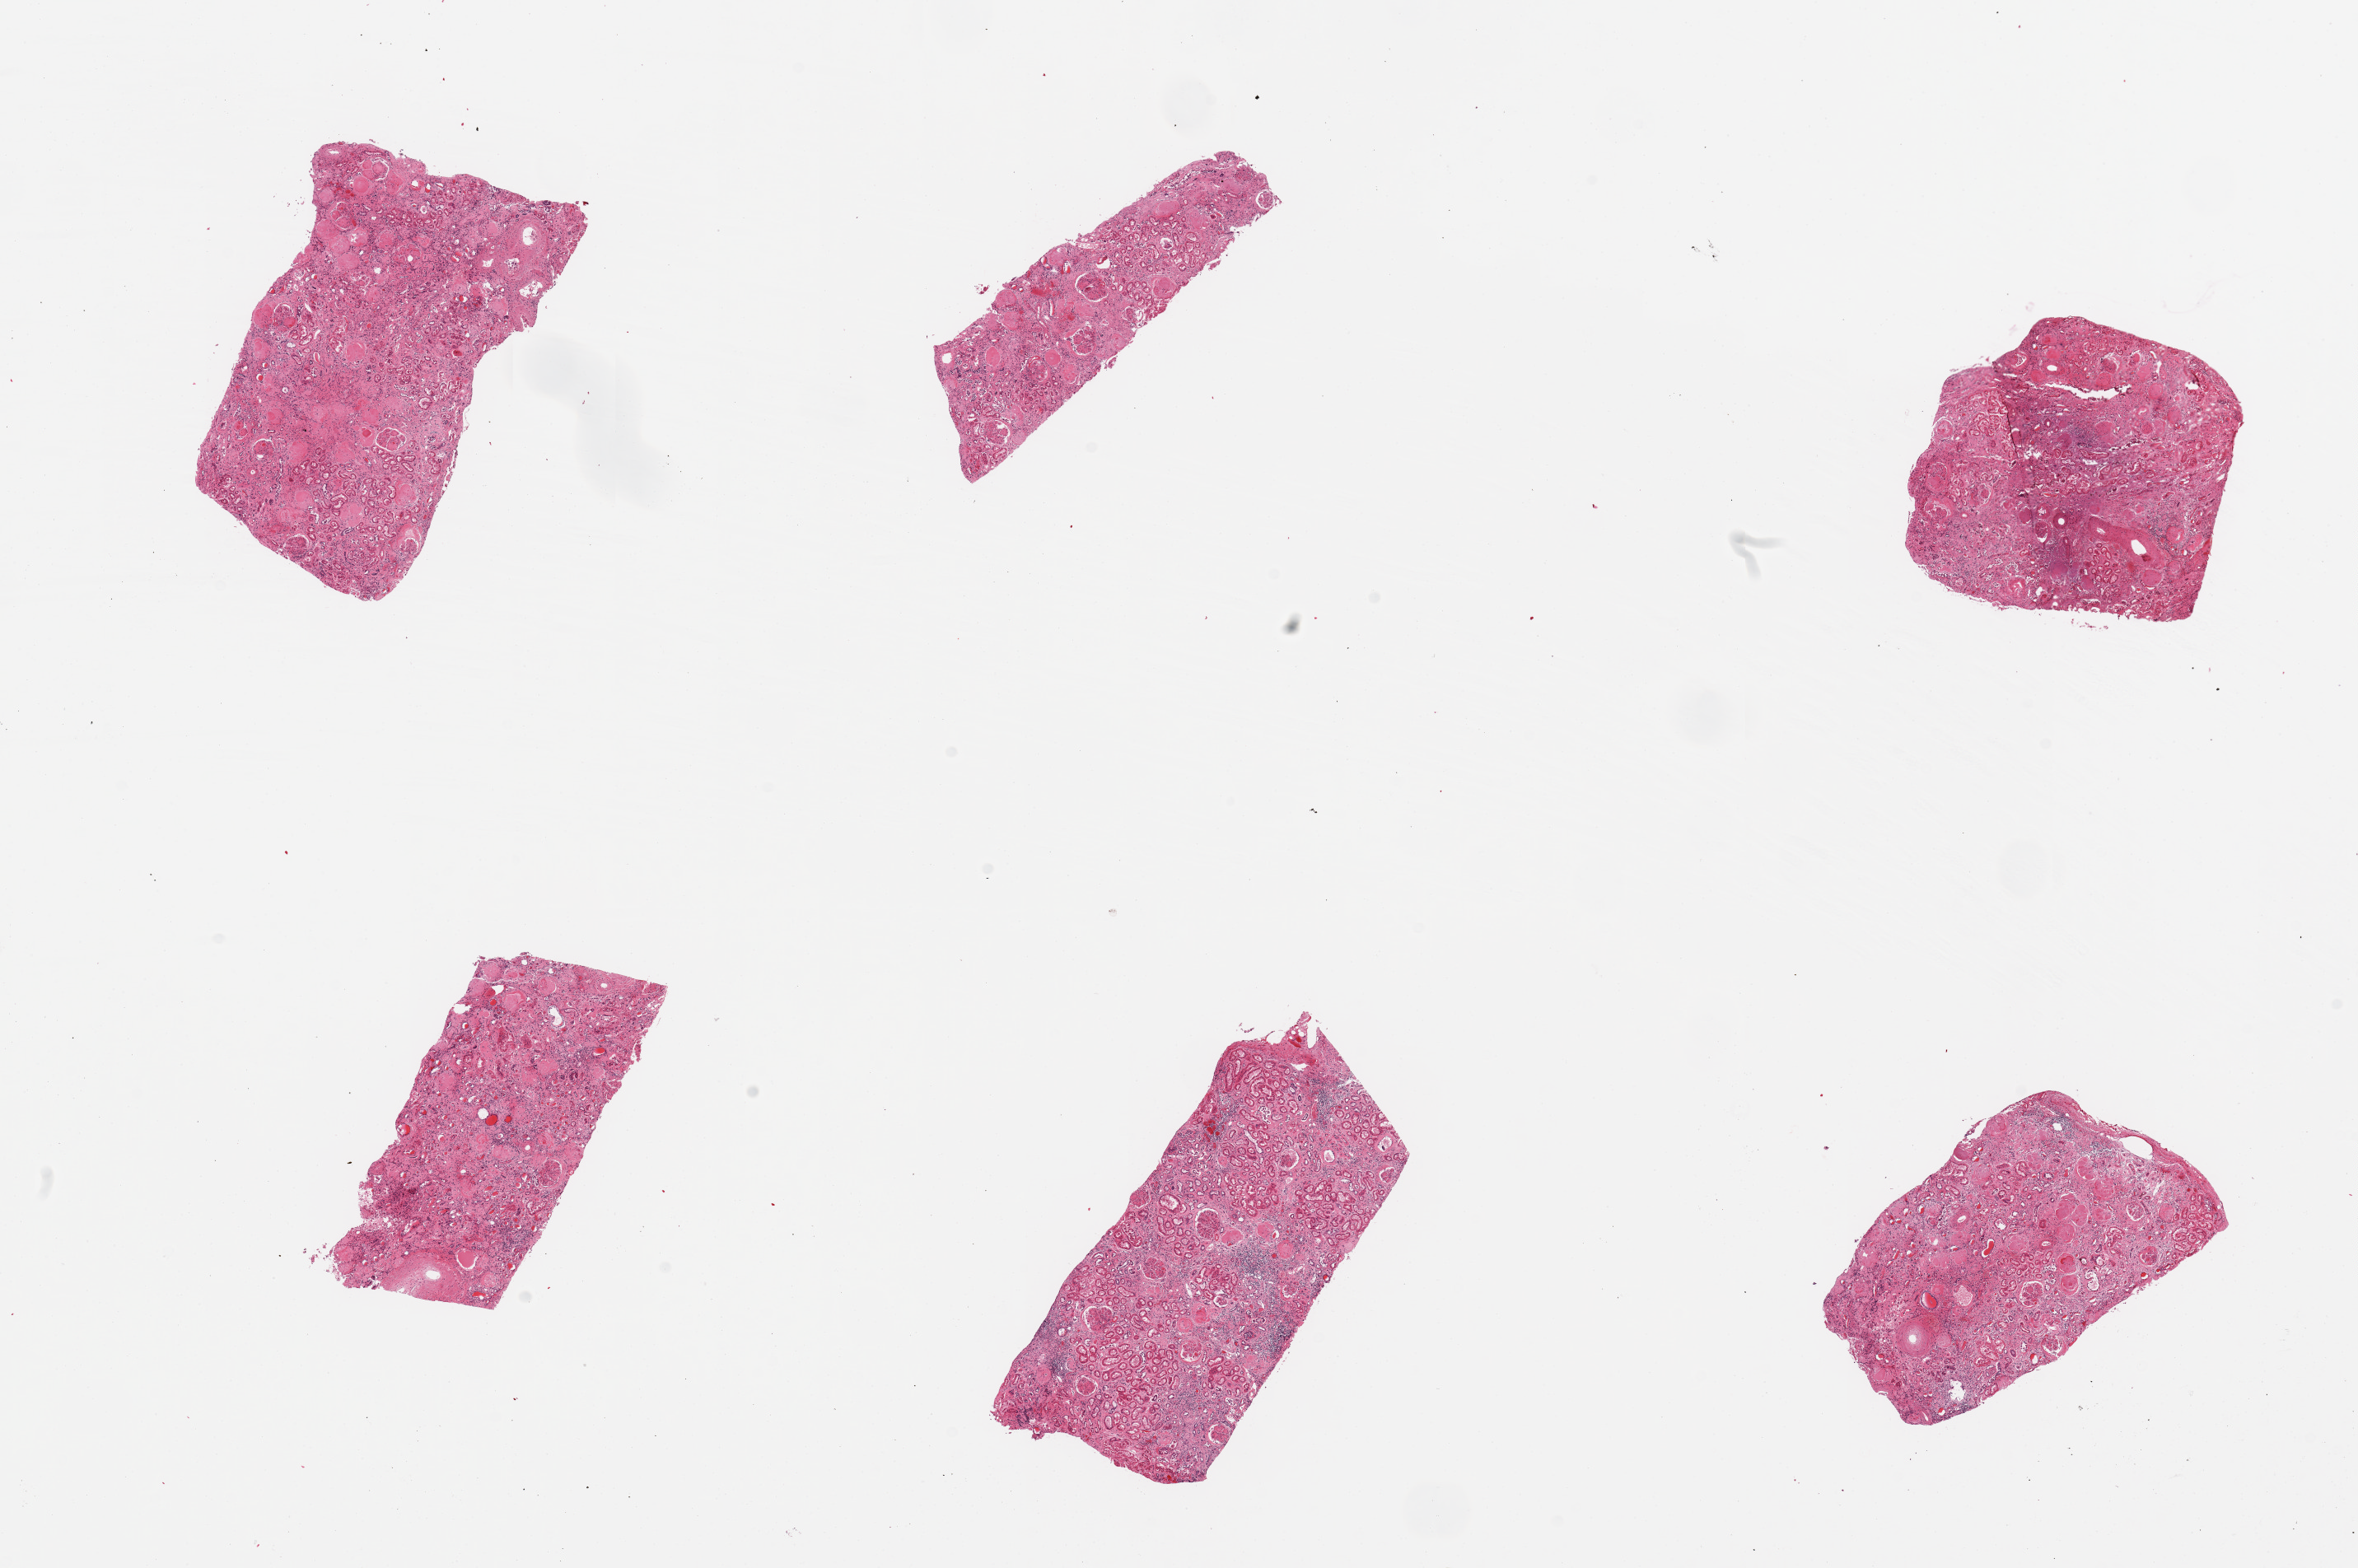
Hematoxylin and eosin (H&E) whole-slide image — a low-resolution overview of the entire scanned area, about 22.6 x 15.1 mm; PAXgene-fixed, paraffin-embedded tissue; sampled site (target tissue): renal cortex; donor tissue sample. Donor sex: female.
• reviewer comment on this tissue sample: 6 pieces; advanced arterio and arteriolonephrosclerosis, significant glomerular sclerosis and hyalinization; diabetic glomerulonephritis